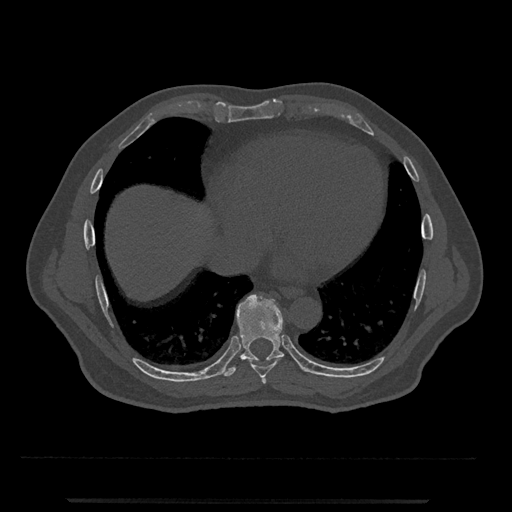
CT including the spine, one axial slice; slice 598 of 797 in the series (ordered by position); reconstruction kernel Br40s/3; 120 kVp; bone window (W 1800 / L 400 HU); 0.5 mm slice thickness; 512 × 512 image matrix, field of view 419 × 419 mm. Male patient, age 63 years. Case-level facts recorded for this patient, not image findings: primary cancer: prostate.
Outlined on this slice (semi-automatically segmented with operator editing):
- T7 vertebra: bounding box <261,376,267,383> (left, top, right, bottom; pixels)
- T8 vertebra: <251,359,279,378>
- T9 vertebra: <220,294,285,377>